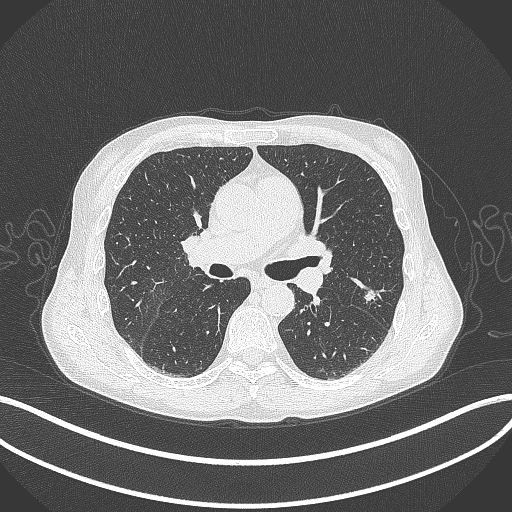
Chest CT, one axial slice. Slice 212 of 429 in the series (ordered by position). Reconstruction kernel B70f. Lung window (W 1500 / L -600 HU). 1 mm slice thickness. 512 × 512 image matrix. Male patient, age 58 years. From the clinical record (not read from this slice): clinical TNM (as recorded): T1c N0 M0; histopathological grade: G2.
Structures marked on this image (rectangle marked by the reading radiologist):
- lung tumour (recorded histology: adenocarcinoma): bounding box <363,286,380,307> (left, top, right, bottom; pixels)